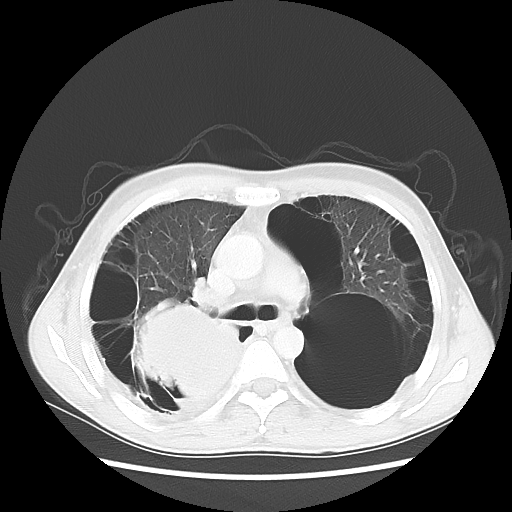
Chest CT, one axial slice. Slice 36 of 57 in the series (ordered by position). Reconstruction kernel LUNG. 140 kVp. Lung window (W 1500 / L -600 HU). 512 × 512 image matrix, field of view 351 × 351 mm. Male patient, age 41 years. From the clinical record (not read from this slice): clinical TNM (as recorded): T4 N0 M1a; histopathological grade: G3.
Structures marked on this image (rectangle marked by the reading radiologist):
- lung tumour (recorded histology: large cell carcinoma): bounding box [x1, y1, x2, y2] px = [130, 295, 244, 411]